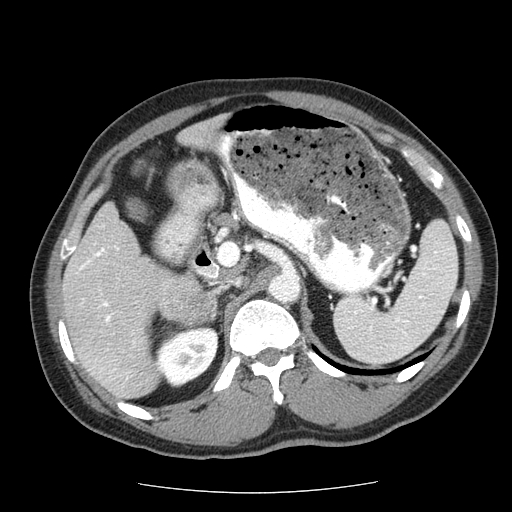
Contrast-enhanced abdominal CT (liver protocol), one axial slice. Position 28 of 85 along the scan axis. 120 kVp. Soft-tissue window (W 400 / L 40 HU). 2.5 mm slice thickness. 512 × 512 image matrix, field of view 360 × 360 mm. Case-level facts recorded for this patient, not image findings: diagnosis: hepatocellular carcinoma (patient treated with transarterial chemoembolisation; whether this scan precedes or follows treatment is not stated here); TNM stage (as recorded): Stage-IIIA; Child-Pugh class: A; tumour differentiation: well differentiated; tumour nodularity: multinodular.
Annotated regions visible in this slice (semi-automatically segmented with operator editing):
- liver parenchyma outside the tumour (the mass and vessels are separate outlines, so this box may not span the whole liver): bounding box [x1, y1, x2, y2] px = [62, 202, 215, 398]
- mass: [160, 277, 210, 323]
- liver vessels: [79, 246, 135, 380]